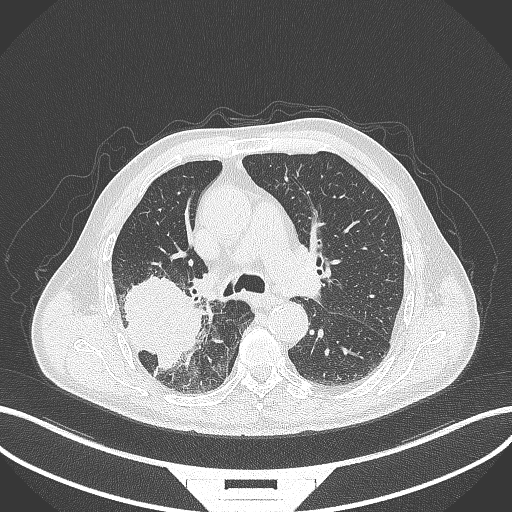
Chest CT, one axial slice. Position 260 of 429 along the scan axis. Reconstruction kernel B70f. 120 kVp. Lung window (W 1500 / L -600 HU). 1 mm slice thickness. 512 × 512 image matrix. Patient: male, 72 years. Case-level facts recorded for this patient, not image findings: clinical TNM (as recorded): T3 N2 M0.
Outlined on this slice (bounding box drawn by a radiologist):
- lung tumour (recorded histology: adenocarcinoma): bounding box (x1, y1, x2, y2) in pixels: (118, 271, 207, 374)